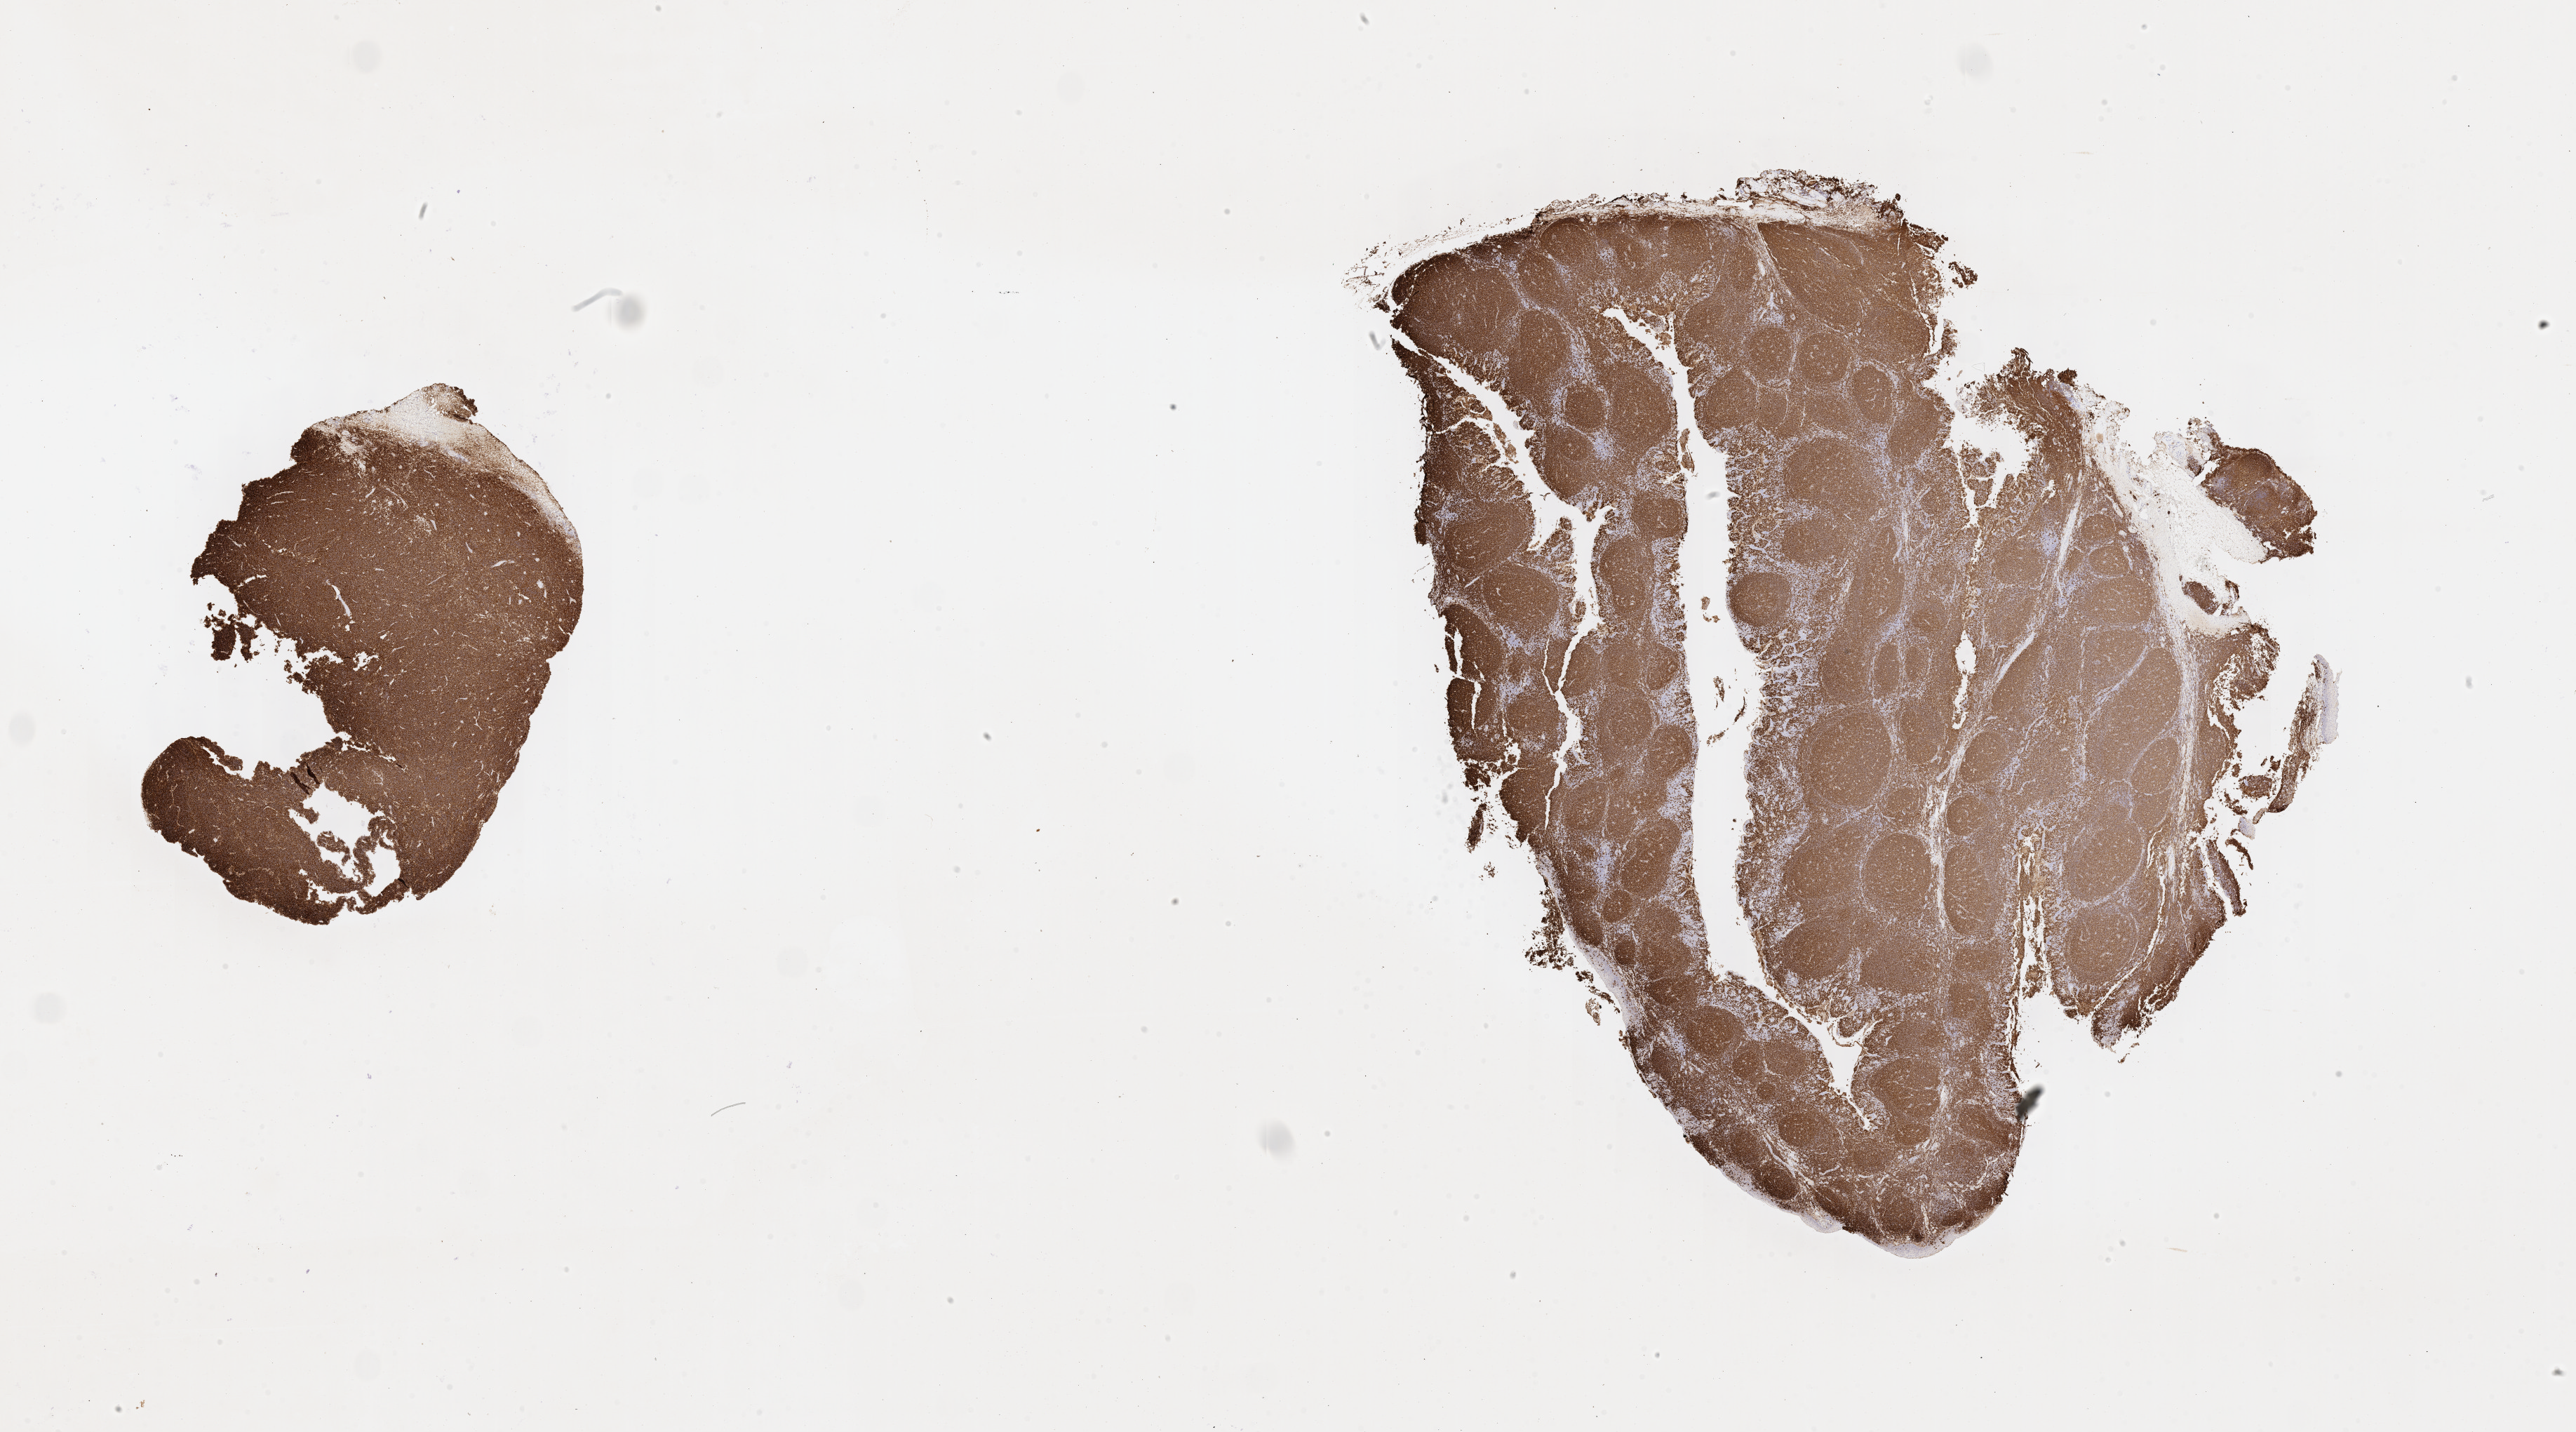
IHC for CD20, whole-slide image, shown as a low-resolution overview of the whole scanned area (about 29.7 x 16.5 mm). Tumor tissue. Anatomic site: mandible. Female patient; age at initial diagnosis 7 years.
Histologic diagnosis: Burkitt lymphoma, NOS.